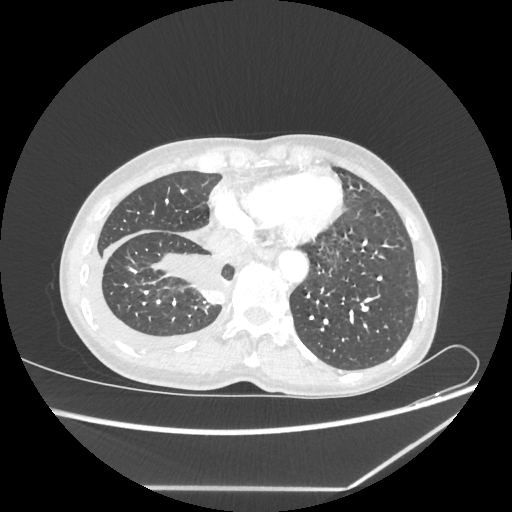
Chest CT, one axial slice; position 60 of 237 along the scan axis; reconstruction kernel STANDARD; 80 kVp; lung window (W 1500 / L -600 HU); 1.25 mm slice thickness; 512 × 512 image matrix. Female patient, age 59 years. Case-level facts recorded for this patient, not image findings: clinical TNM (as recorded): T1c N1 M1.
Outlined on this slice (bounding box drawn by a radiologist):
- lung tumour (recorded histology: adenocarcinoma): bounding box [x1, y1, x2, y2] px = [197, 288, 228, 306]